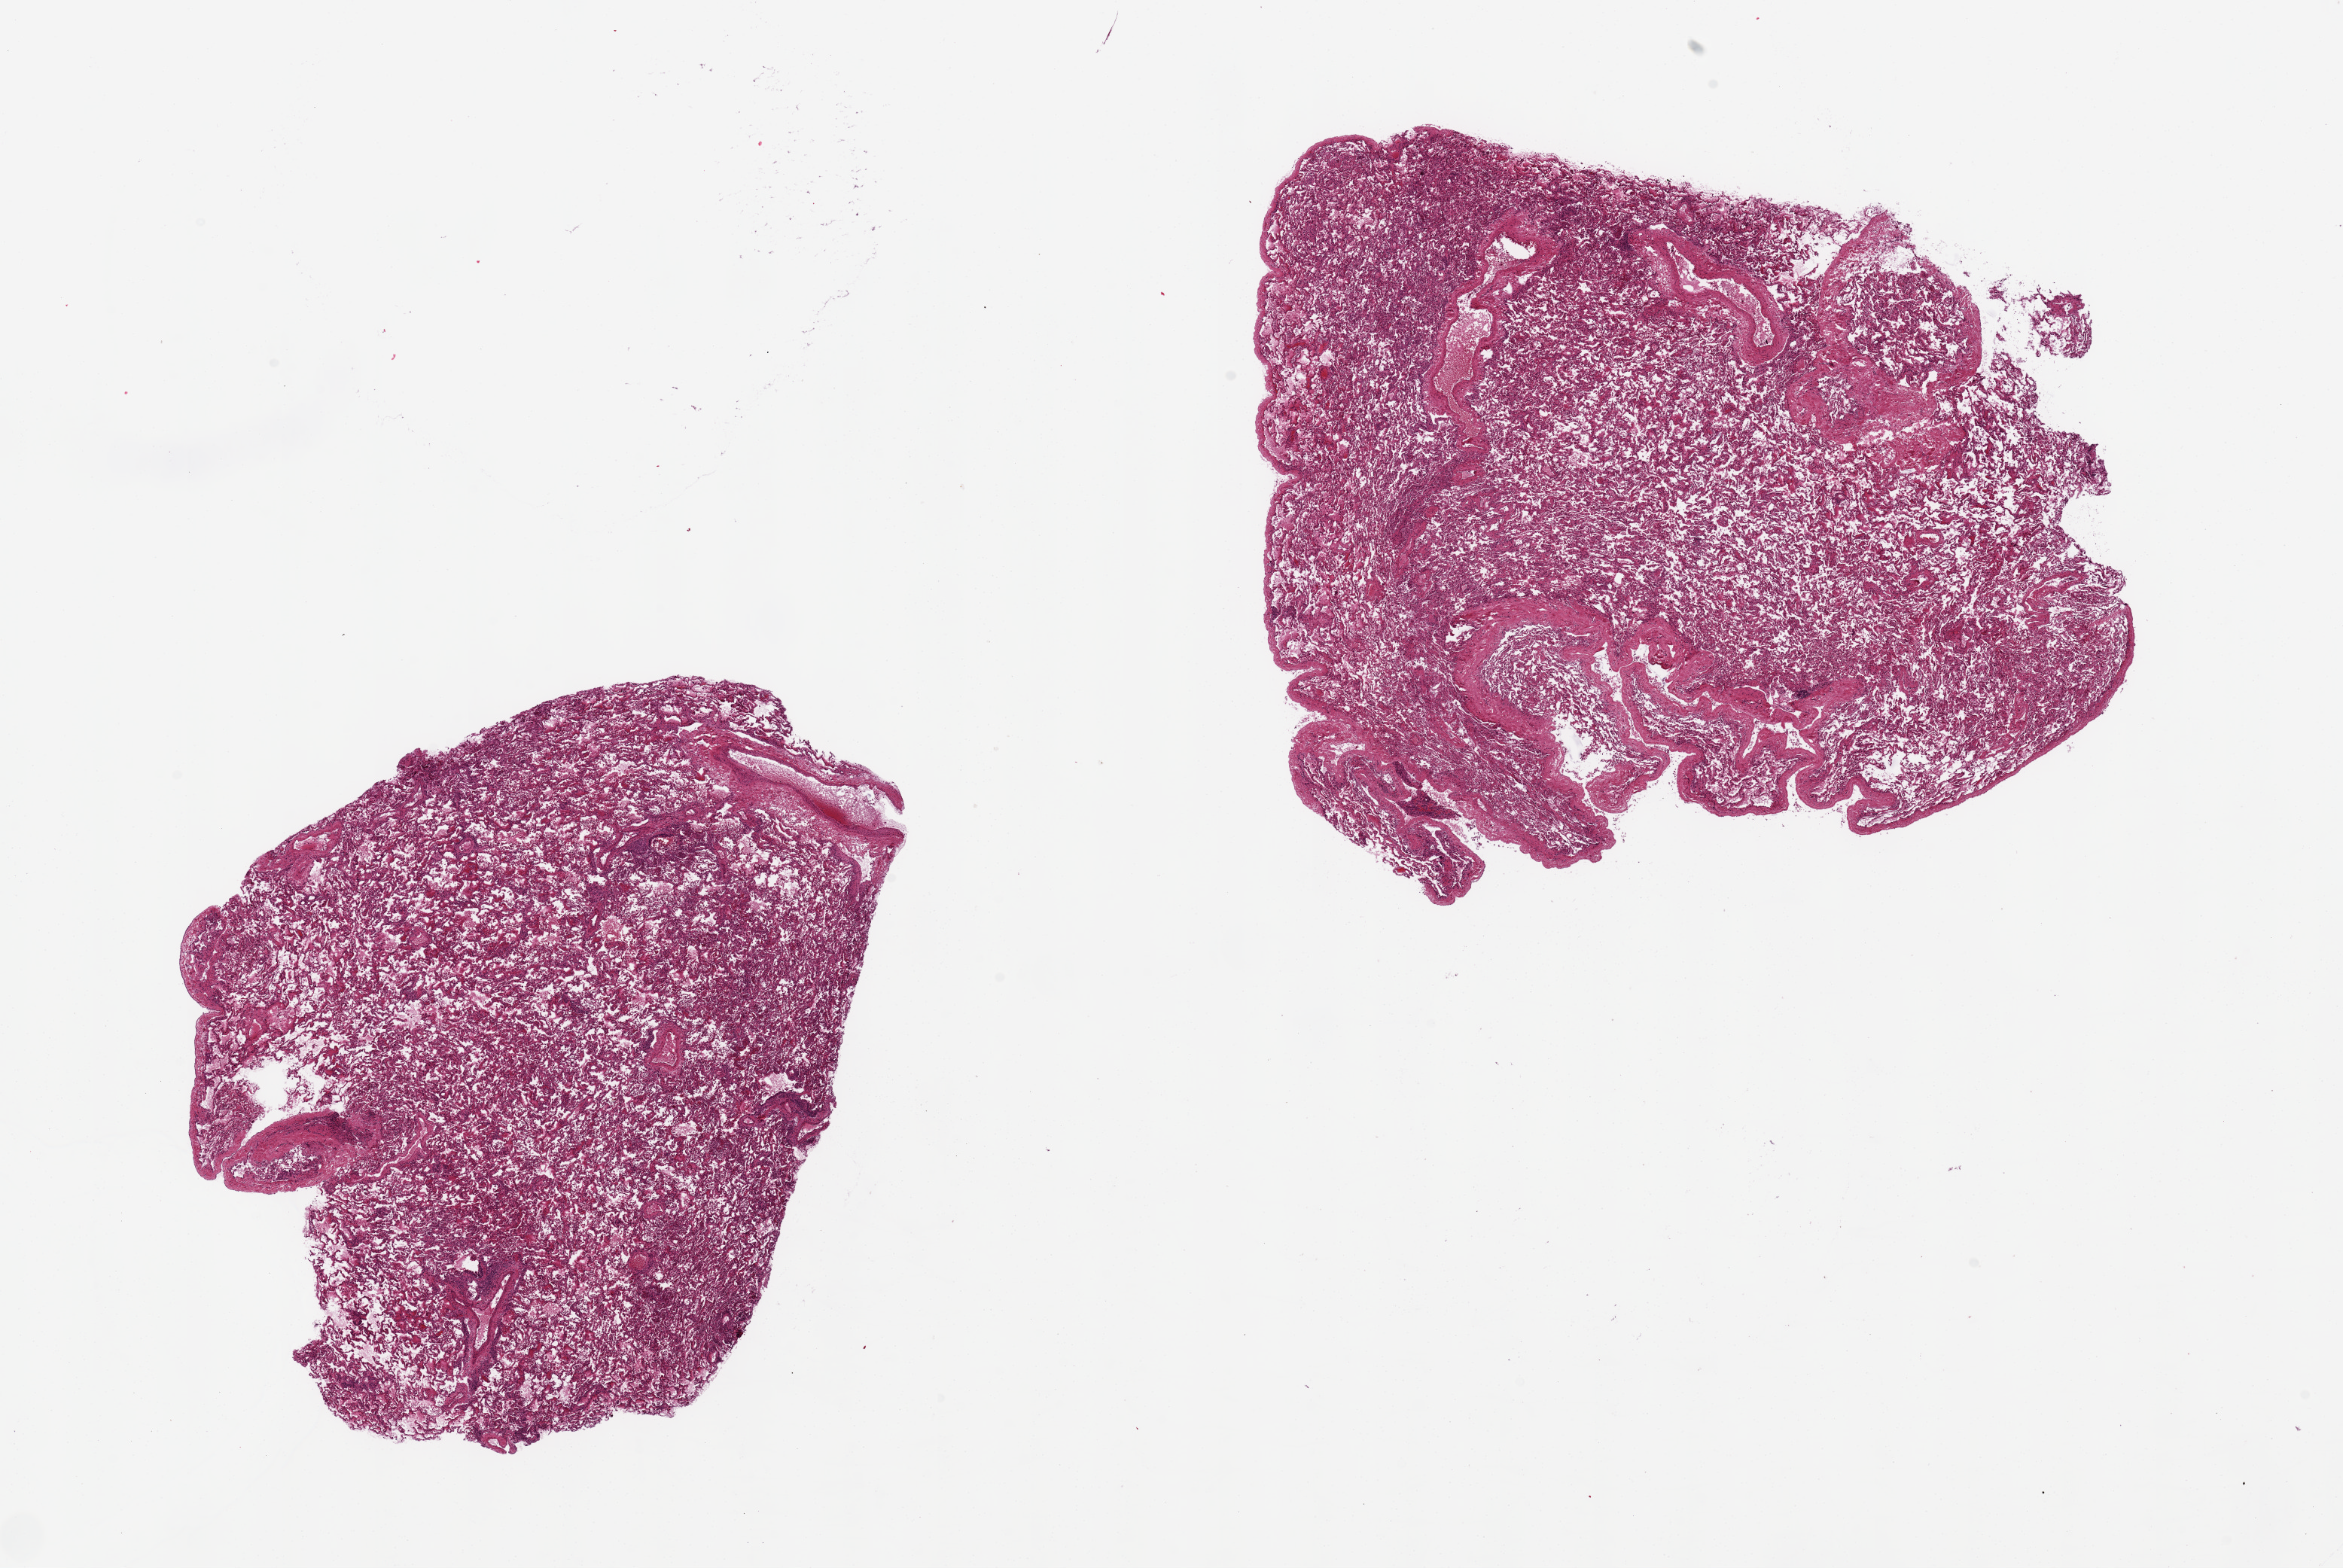
Digitized haematoxylin and eosin-stained section, brightfield, a low-resolution overview of the entire scanned area, about 24.6 x 16.5 mm (acquisition: 20x scan), PAXgene-fixed paraffin-embedded (PFPE) section, section of lung (target tissue), donor tissue sample. Donor sex: female.
- review note (as recorded): 2 pieces, ~10x8 & 7x7mm; bronchopneumonia and alveolar desquamation